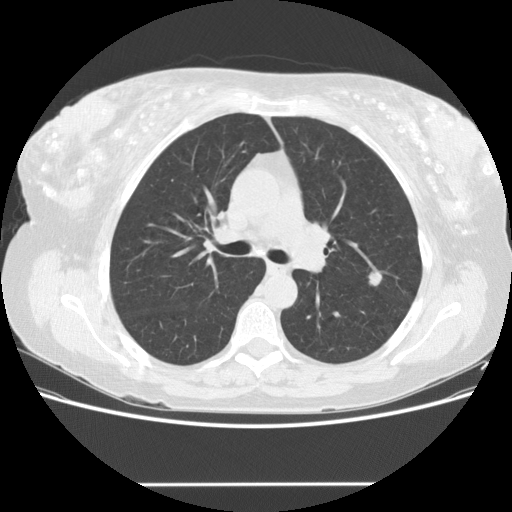
Chest CT (low-dose screening protocol), one axial image. Second screening round (one year after baseline). Lung window (W 1500 / L -600 HU). 120 kVp. 512 × 512 image matrix, field of view 360 × 360 mm. Female participant, aged 57 years at enrolment. Current smoker at enrolment.
• Lesion marked by an expert reader, box from (x=358, y=266) to (x=390, y=294) px.
• Screening reader's record for this exam (one nodule recorded; not confirmed to be the boxed lesion): non-calcified nodule or mass ≥4 mm, lingula, 10 × 8 mm, smooth margins, soft tissue attenuation, pre-existing on the prior screen: no.
• Official screen result: positive, other.